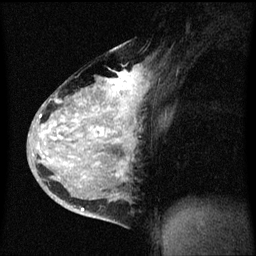
Breast MRI (dynamic contrast-enhanced), one sagittal slice. Position 38 of 60 along the scan axis. Dynamic contrast-enhanced series, image 2 of 3 at this slice position (ordered by acquisition). 1.5 T. TE 4.2 ms, TR 8.4 ms. 2 mm slice thickness. 256 × 256 image matrix, field of view 200 × 200 mm. Patient: female, 34 years. Case-level facts recorded for this patient, not image findings: setting: breast cancer imaged before/during neoadjuvant chemotherapy; receptor status: HR-positive, HER2-negative.
Annotated regions visible in this slice (semi-automatically segmented with operator editing):
- analysis volume of interest (the breast-tissue region the enhancement analysis was run in; not a lesion): bounding box [x1, y1, x2, y2] px = [34, 48, 145, 215]
- tumour enhancement mask (voxels above the 70 % enhancement threshold inside the analysis volume of interest): [40, 72, 139, 211]